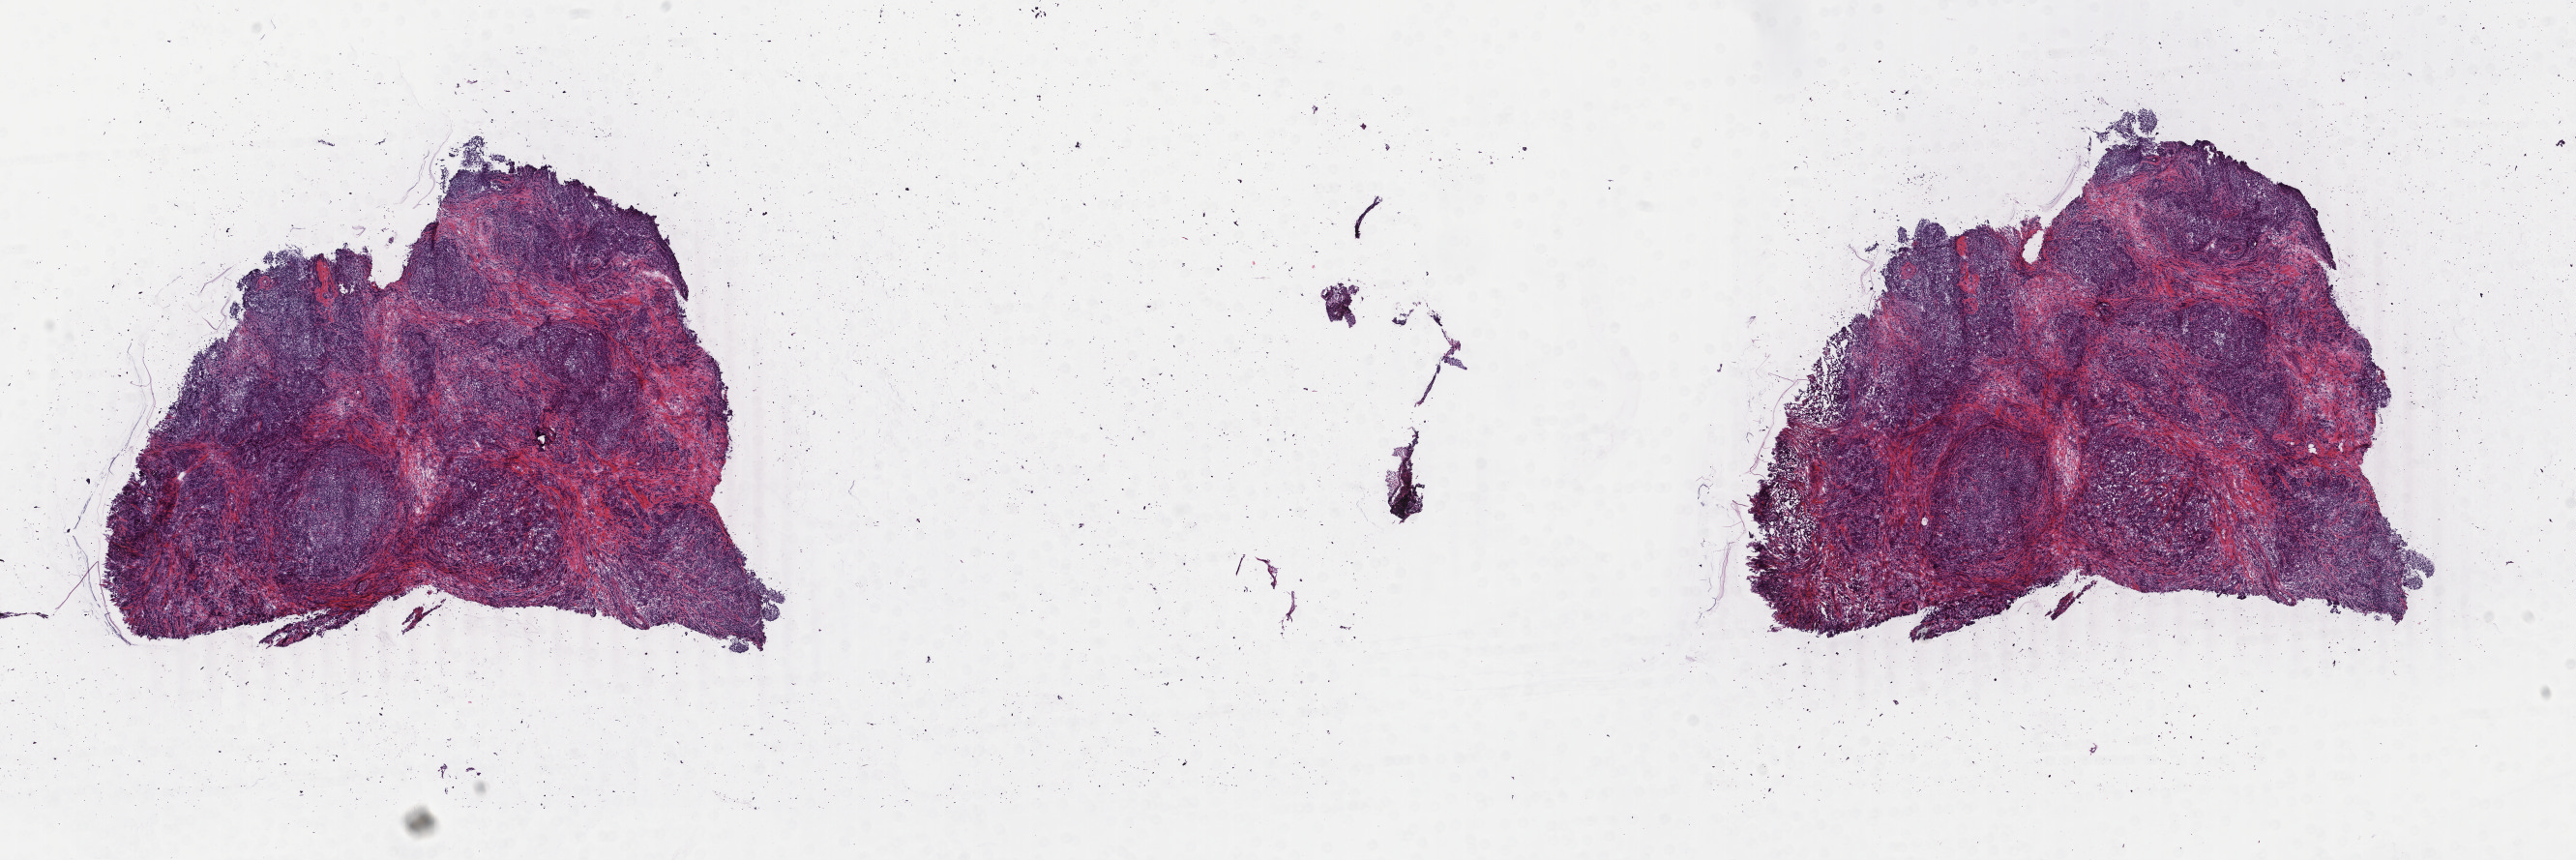
H&E-stained whole-slide image — shown as a low-resolution overview of the whole scanned area (about 21.2 x 7.1 mm, from a 40x scan); frozen section from the top of the tissue portion; primary tumour sample from the breast. Female patient; age at initial diagnosis 65 years. Pathologist review of this section (percent, as recorded): tumour cells 70%, tumour nuclei 70%, normal cells 0%, stromal cells 25%, necrosis 5%. Inflammatory infiltration, as recorded: lymphocyte infiltration 40%, monocyte infiltration 20%, neutrophil infiltration 20%.
Diagnosis: Infiltrating duct carcinoma, NOS. Lymph nodes positive (case pathology): 0 of 1 examined. Laterality: left. AJCC pathologic stage: IIA (6th edition).